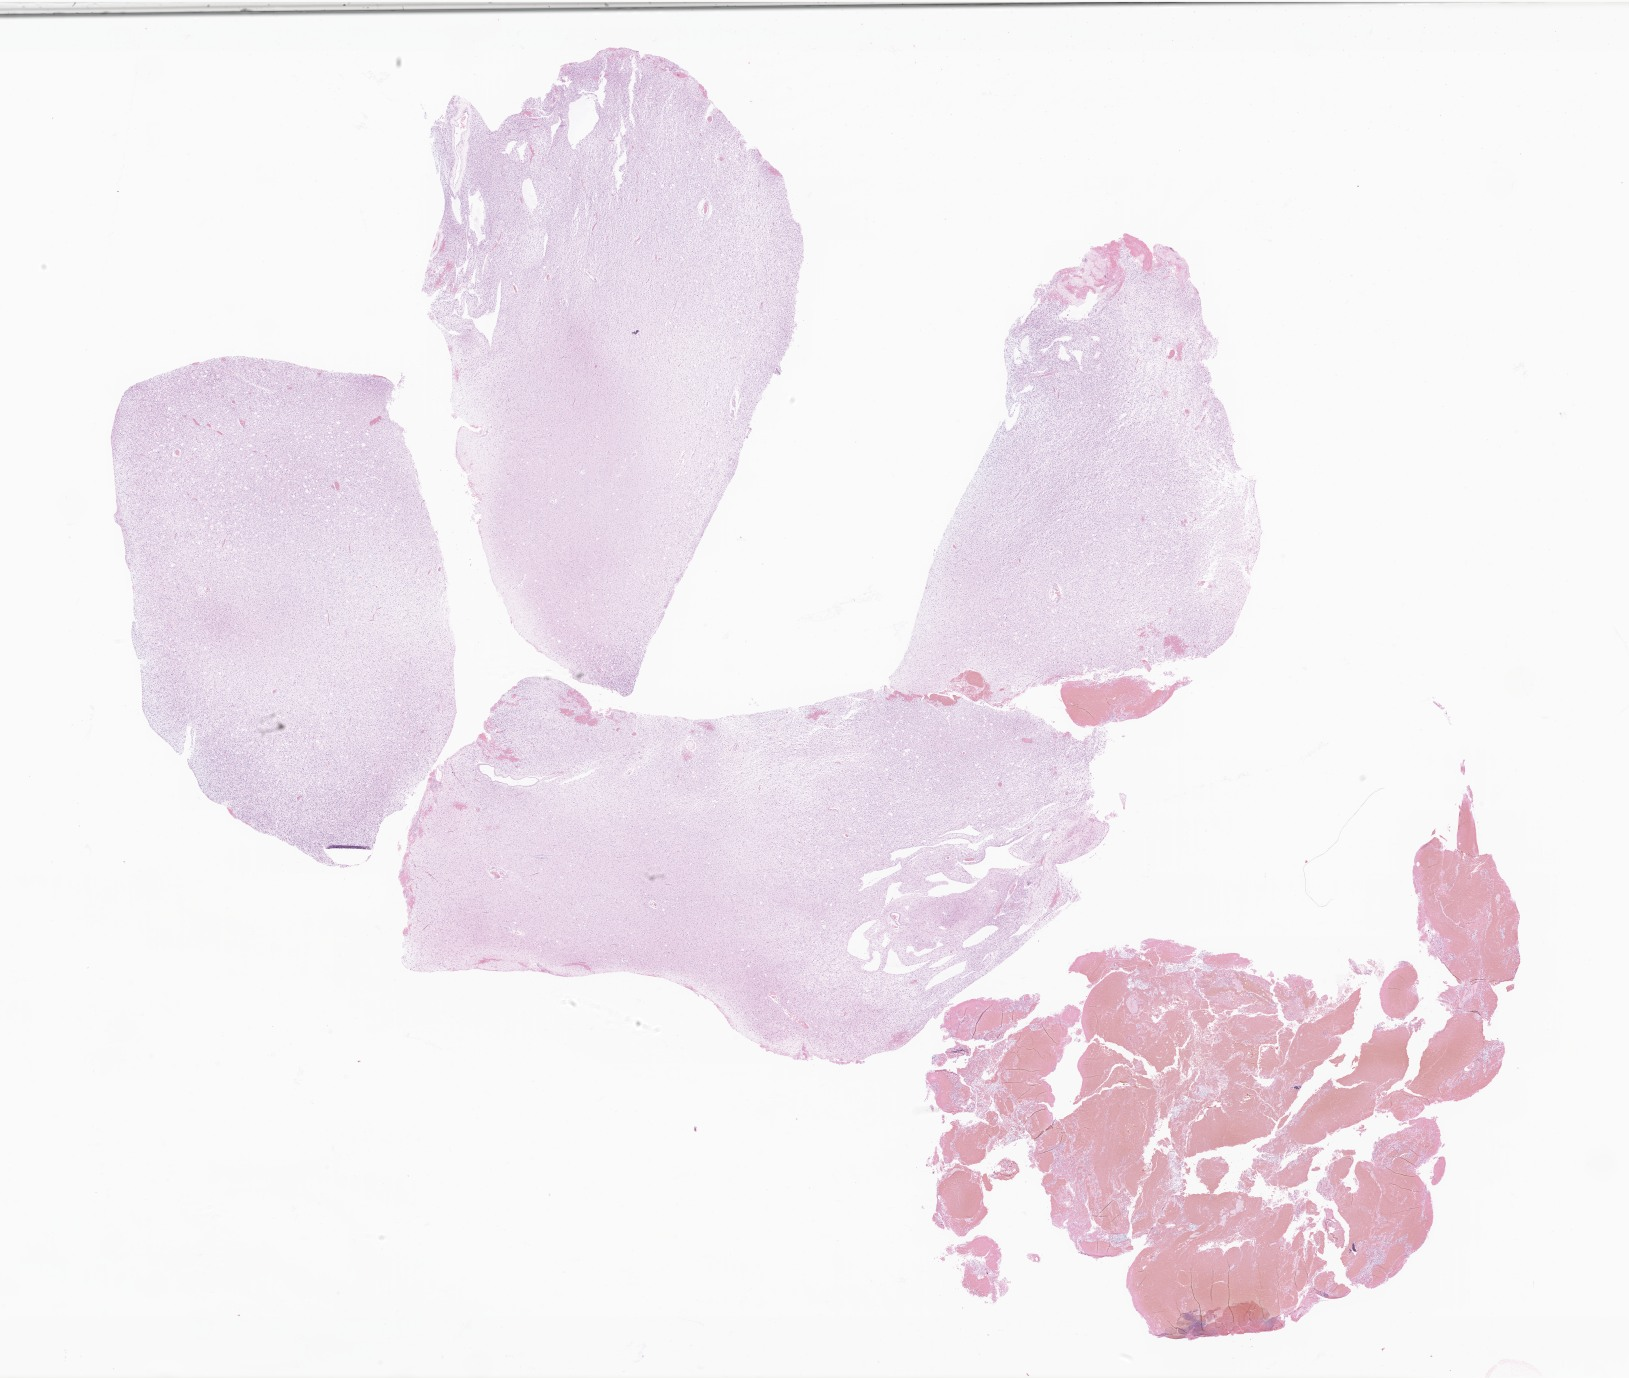
Whole-slide image, H&E stain of tumor tissue from the parietal lobe, whole scanned area (about 27.5 x 23.2 mm) shown as a low-resolution overview, FFPE section. Patient female; age 213 months.
Recorded diagnosis: Astrocytoma, NOS.